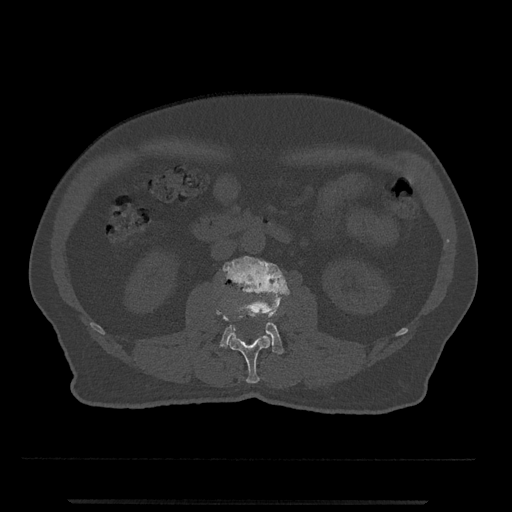
CT including the spine, one axial slice; slice 238 of 797 in the series (ordered by position); bone window (W 1800 / L 400 HU); 0.5 mm slice thickness; 512 × 512 image matrix, field of view 419 × 419 mm. Male patient, age 63 years. From the clinical record (not read from this slice): primary cancer: prostate.
Structures marked on this image (semi-automatic segmentation, software-assisted and operator-edited):
- L2 vertebra: bounding box [x1, y1, x2, y2] px = [216, 291, 274, 383]
- L3 vertebra: [218, 256, 290, 354]